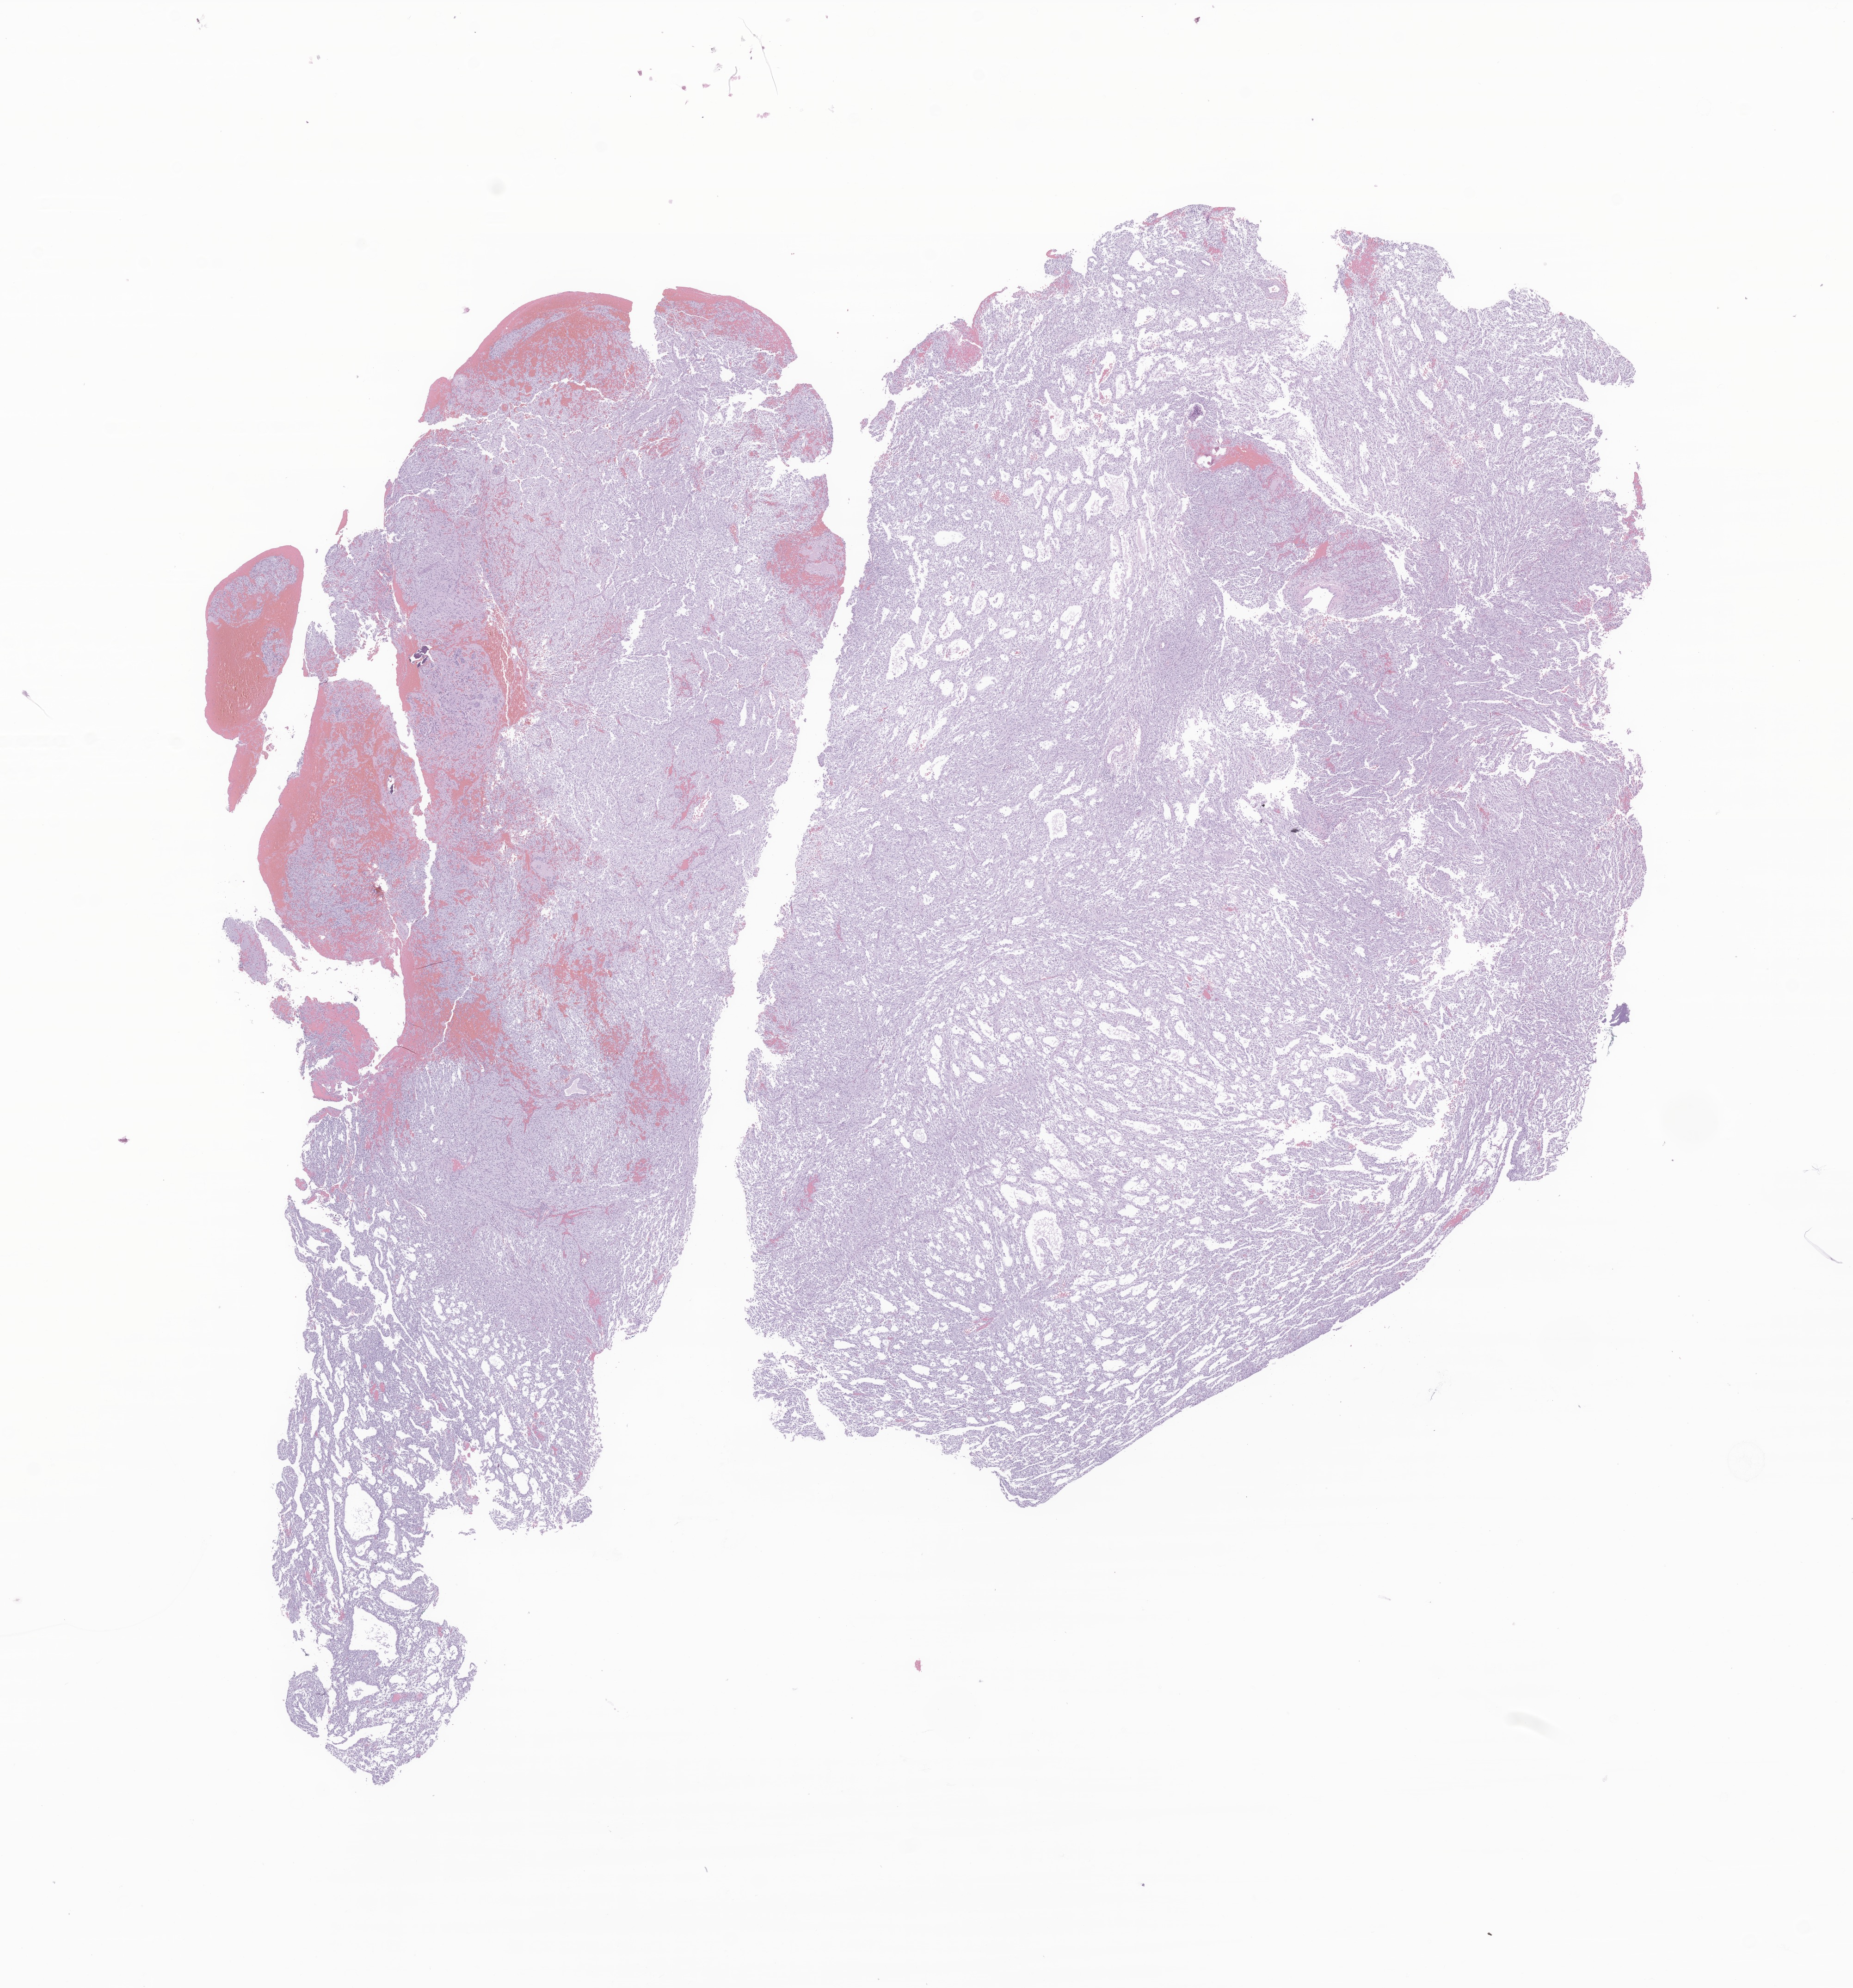
Whole-slide image, hematoxylin and eosin (H&E) stain of tumor tissue from the parietal lobe — a low-resolution overview of the entire scanned area, about 16.9 x 18.1 mm. FFPE section. Female patient, age 194 months.
Recorded diagnosis: Glioma, malignant.